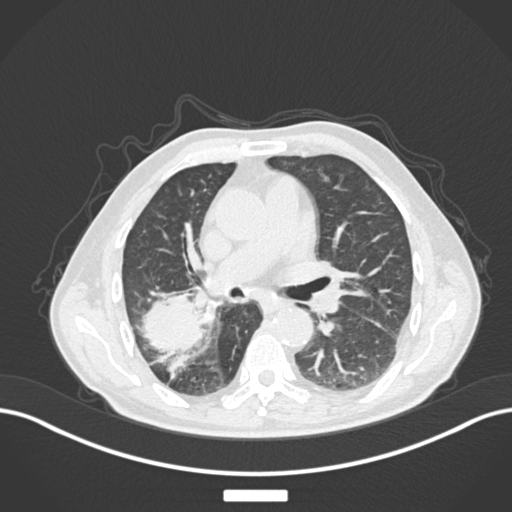
Chest CT, one axial slice. Reconstruction kernel B30f. 120 kVp. Lung window (W 1500 / L -600 HU). 1 mm slice thickness. 512 × 512 image matrix, field of view 400 × 400 mm. Patient: male, 72 years. Case-level facts recorded for this patient, not image findings: clinical TNM (as recorded): T3 N2 M0.
Outlined on this slice (bounding box drawn by a radiologist):
- lung tumour (recorded histology: adenocarcinoma): bounding box [x1, y1, x2, y2] px = [137, 286, 205, 361]